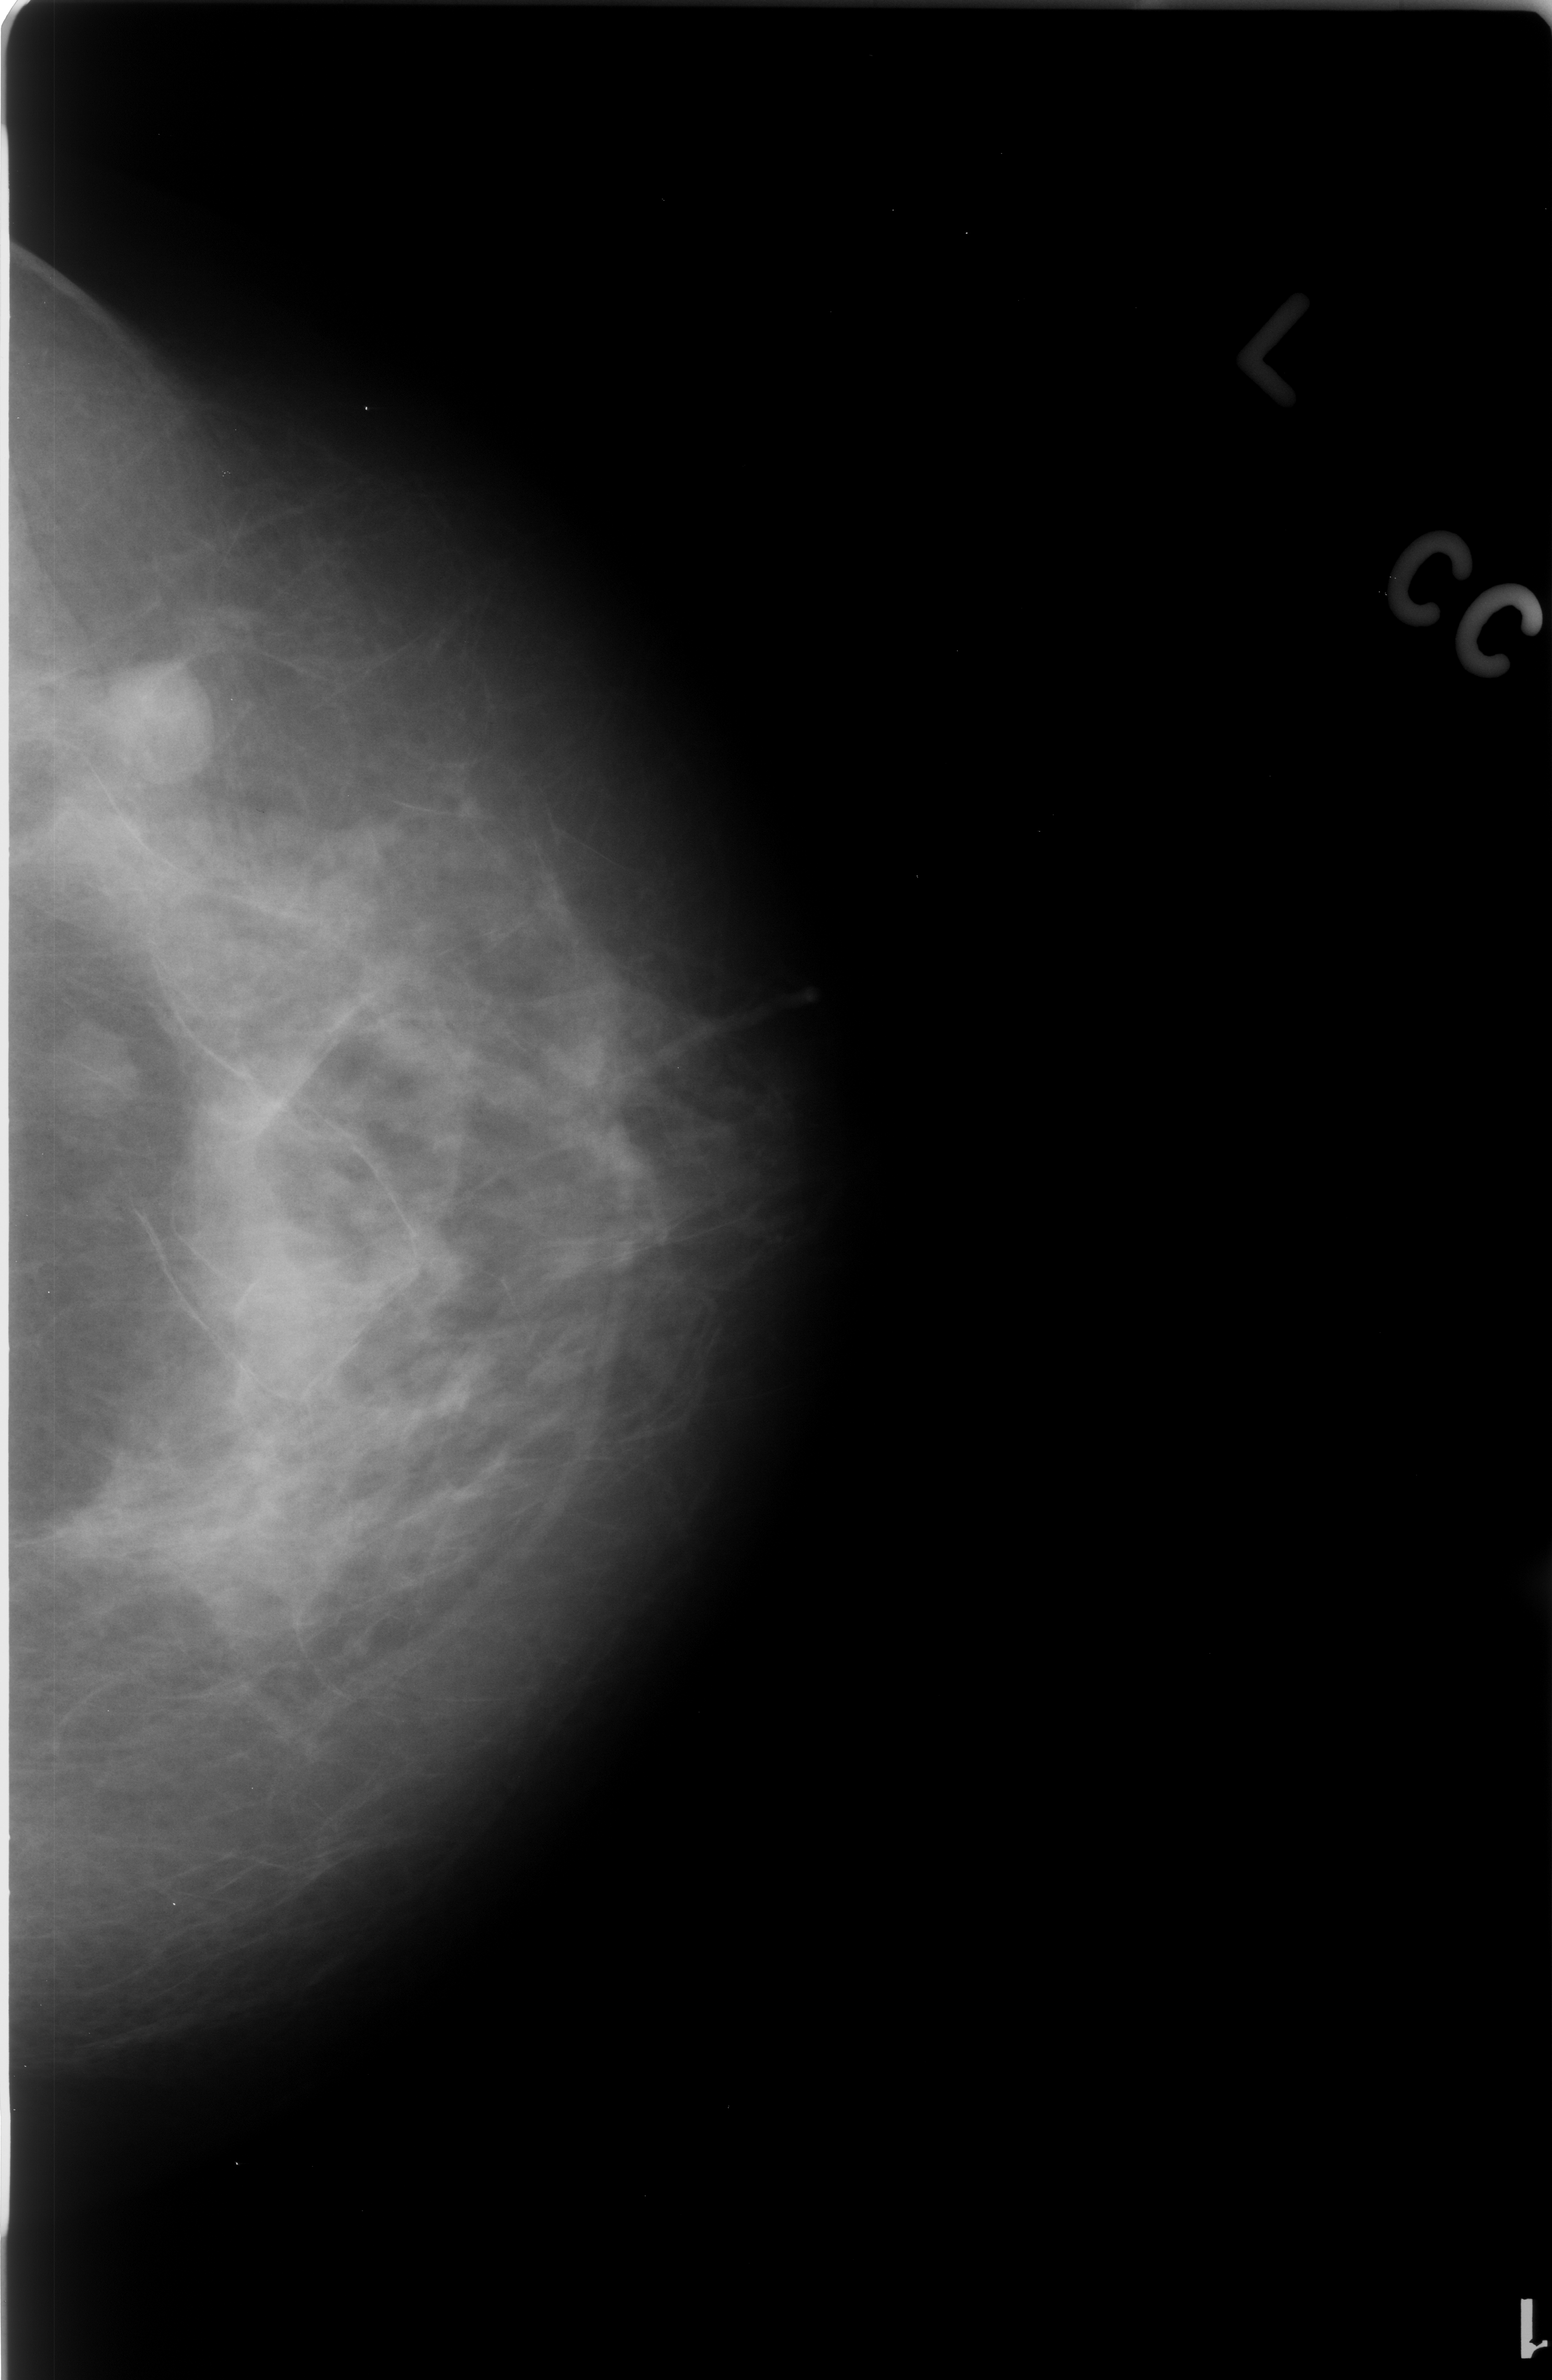
Scanned film-screen mammogram, left breast, CC view, BI-RADS breast density category 2 (scale 1–4).
- Marked findings (only marked abnormalities are described; nothing is implied about the rest of the image): Finding 1 of 2: mass, shape oval, margins circumscribed; BI-RADS assessment category 3; subtlety rating 5 on a 1 (subtle) to 5 (obvious) scale; pathology result (as recorded, not read from the image): benign.
- Finding 2 of 2: mass, shape oval, margins circumscribed; BI-RADS assessment category 3; subtlety rating 5 on a 1 (subtle) to 5 (obvious) scale; pathology result (as recorded, not read from the image): benign.